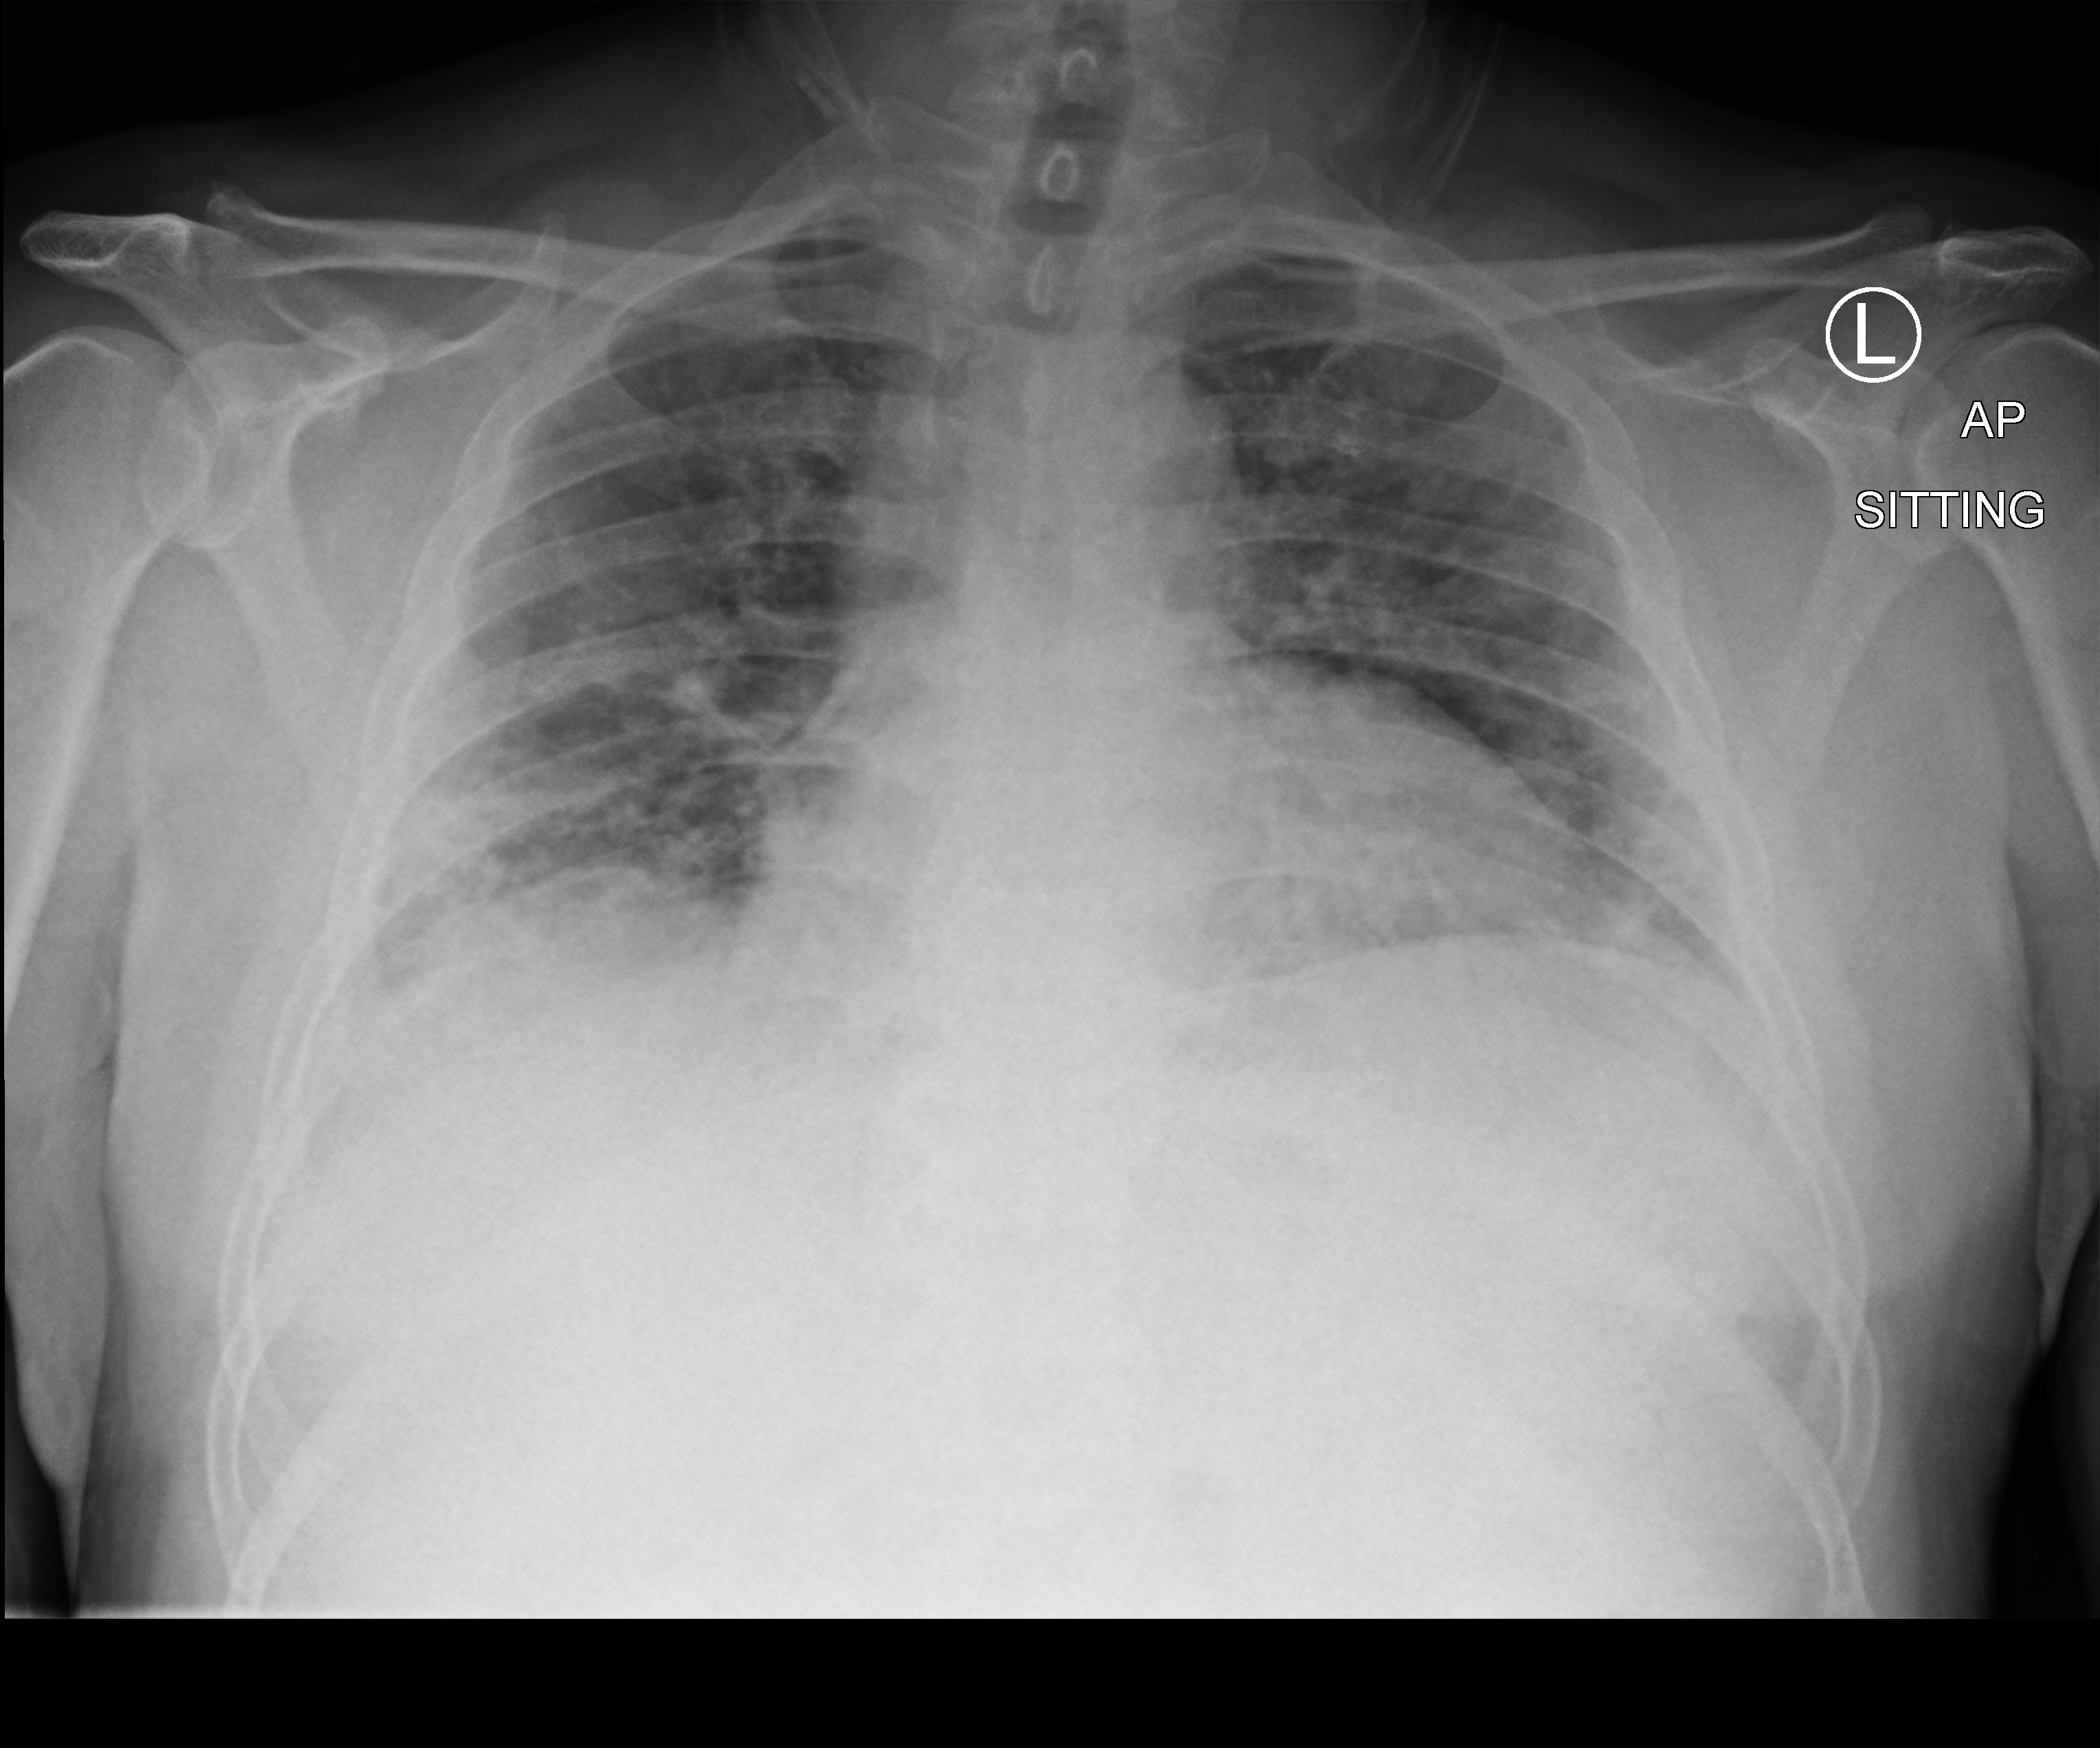
Bedside chest radiograph (computed radiography); anteroposterior (AP) projection. Male patient hospitalised with COVID-19, age 18–59 years.
Admission-level facts for this patient (not findings on this image; timing relative to this image not recorded): diabetes (admission record): yes.